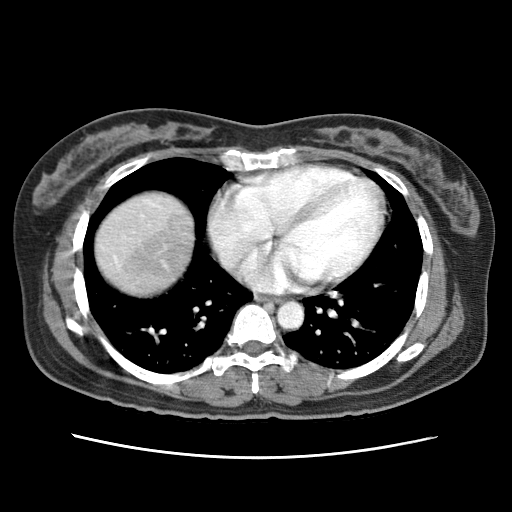
Contrast-enhanced abdominal CT (liver protocol), one axial slice; 120 kVp; soft-tissue window (W 400 / L 40 HU); 2.5 mm slice thickness; 512 × 512 image matrix, field of view 340 × 340 mm. Case-level facts recorded for this patient, not image findings: diagnosis: hepatocellular carcinoma (patient treated with transarterial chemoembolisation; whether this scan precedes or follows treatment is not stated here); TNM stage (as recorded): Stage-I; Child-Pugh class: A; tumour differentiation: moderately differentiated; tumour nodularity: uninodular.
Annotated regions visible in this slice (semi-automatically segmented with operator editing):
- abdominal aorta: bounding box (x1, y1, x2, y2) in pixels: (277, 301, 303, 329)
- liver parenchyma outside the tumour (the mass and vessels are separate outlines, so this box may not span the whole liver): (96, 194, 192, 294)
- liver vessels: (114, 202, 154, 262)